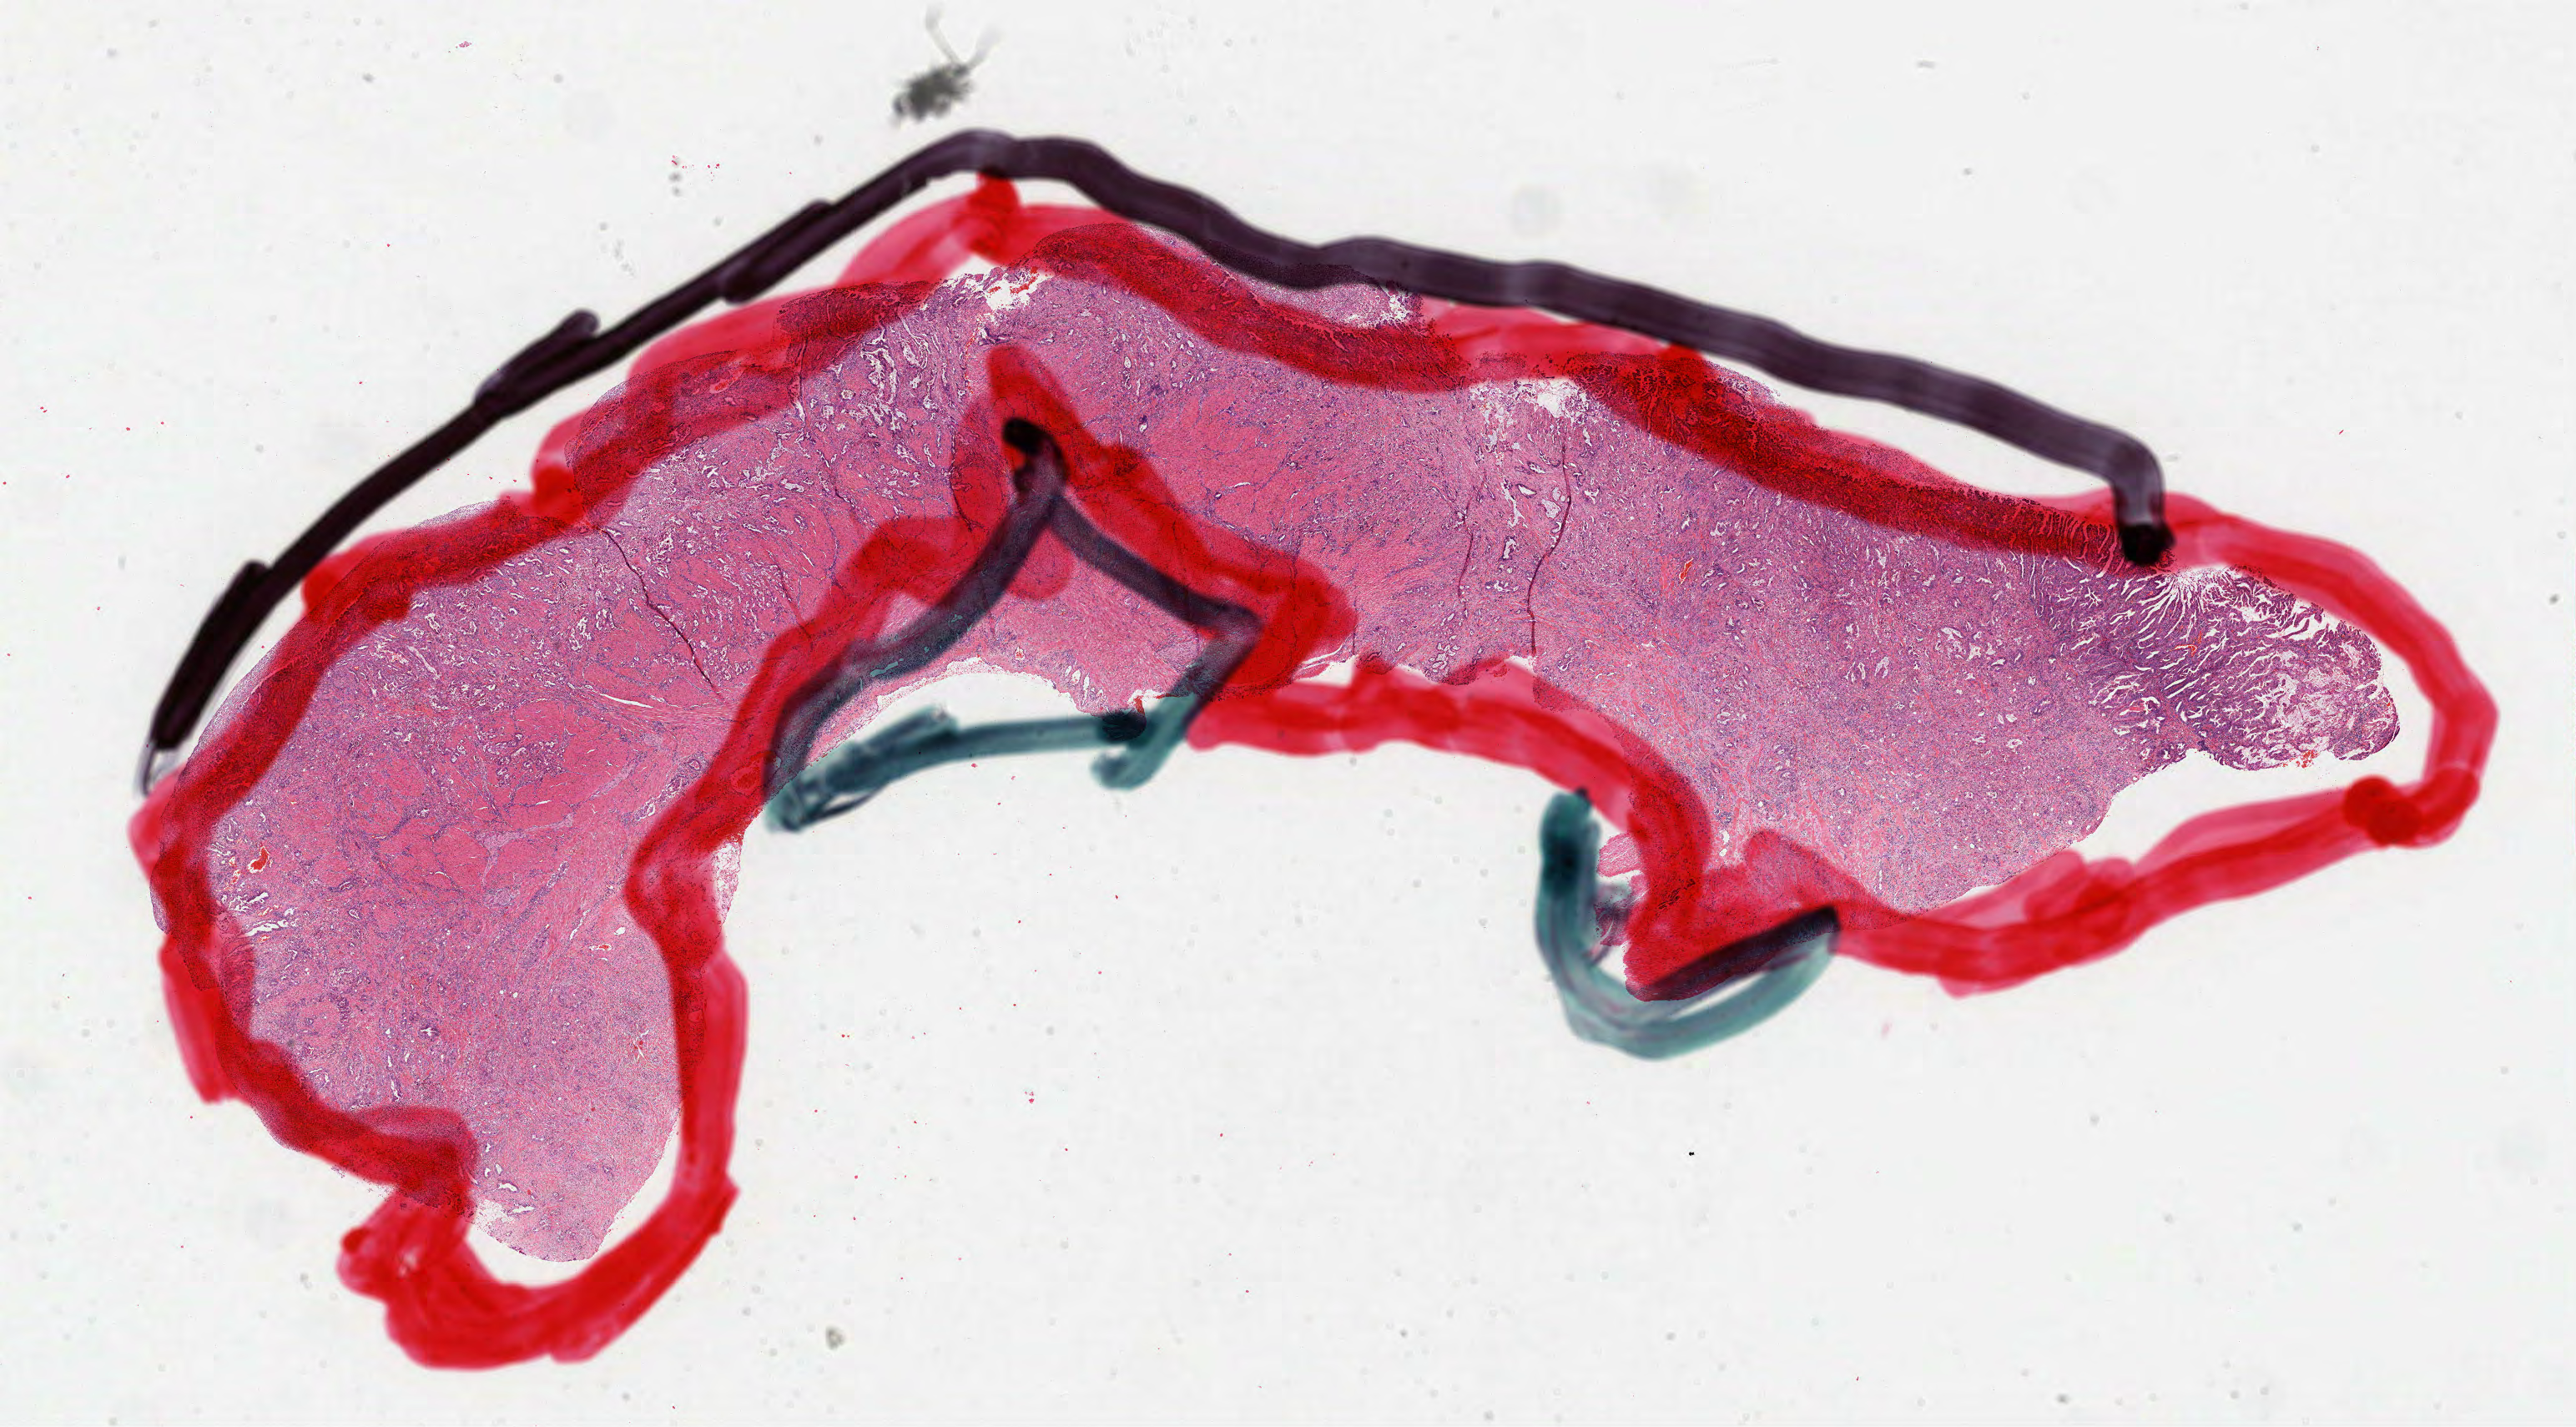
H&E-stained whole-slide image — whole scanned area (about 24.9 x 13.8 mm) shown as a low-resolution overview, formalin-fixed paraffin-embedded (FFPE) diagnostic section, stomach, primary tumour sample. Patient: male, age at initial diagnosis 72 years. Histologic grade: G3 (poorly differentiated).
Lymph nodes positive (case pathology): 1 of 7 examined. Diagnosis: Adenocarcinoma, intestinal type. AJCC pathologic stage: III (7th edition).